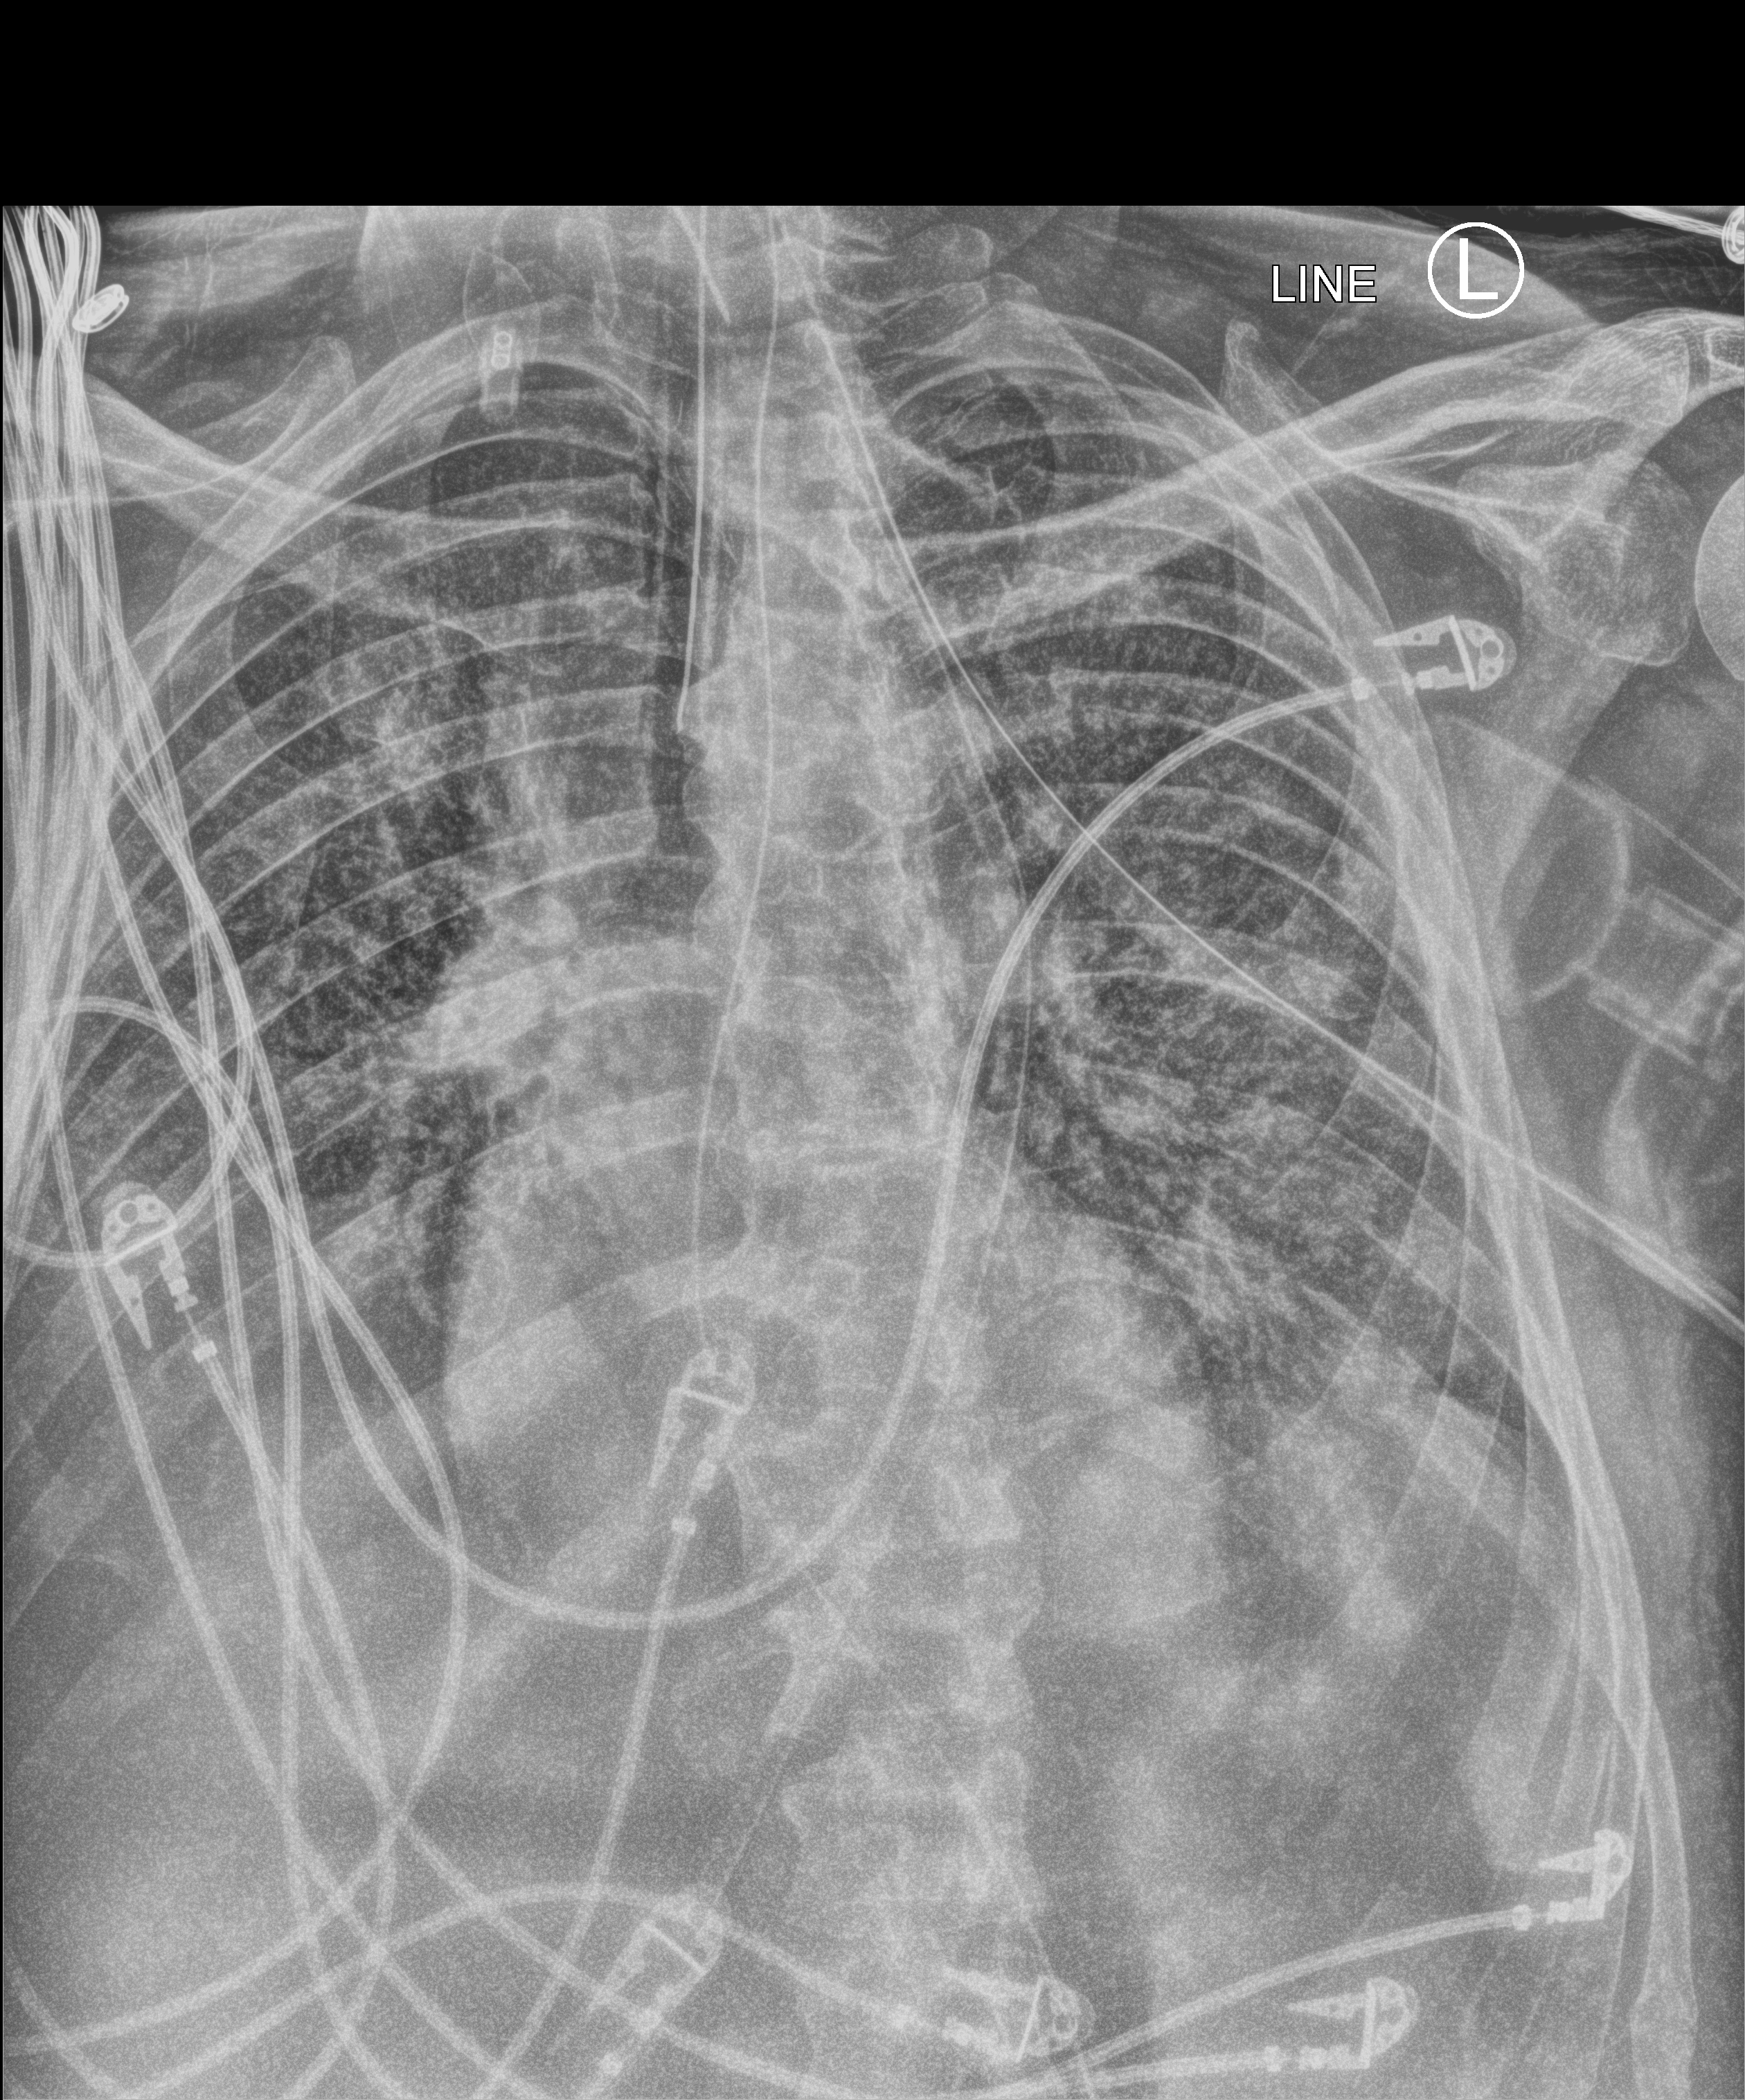
Bedside chest radiograph (computed radiography); anteroposterior (AP) projection. Male patient hospitalised with COVID-19, age 60–74 years.
Hospital-stay facts (about this admission, not read from this image; timing relative to this image not recorded):
- diabetes (admission record): yes